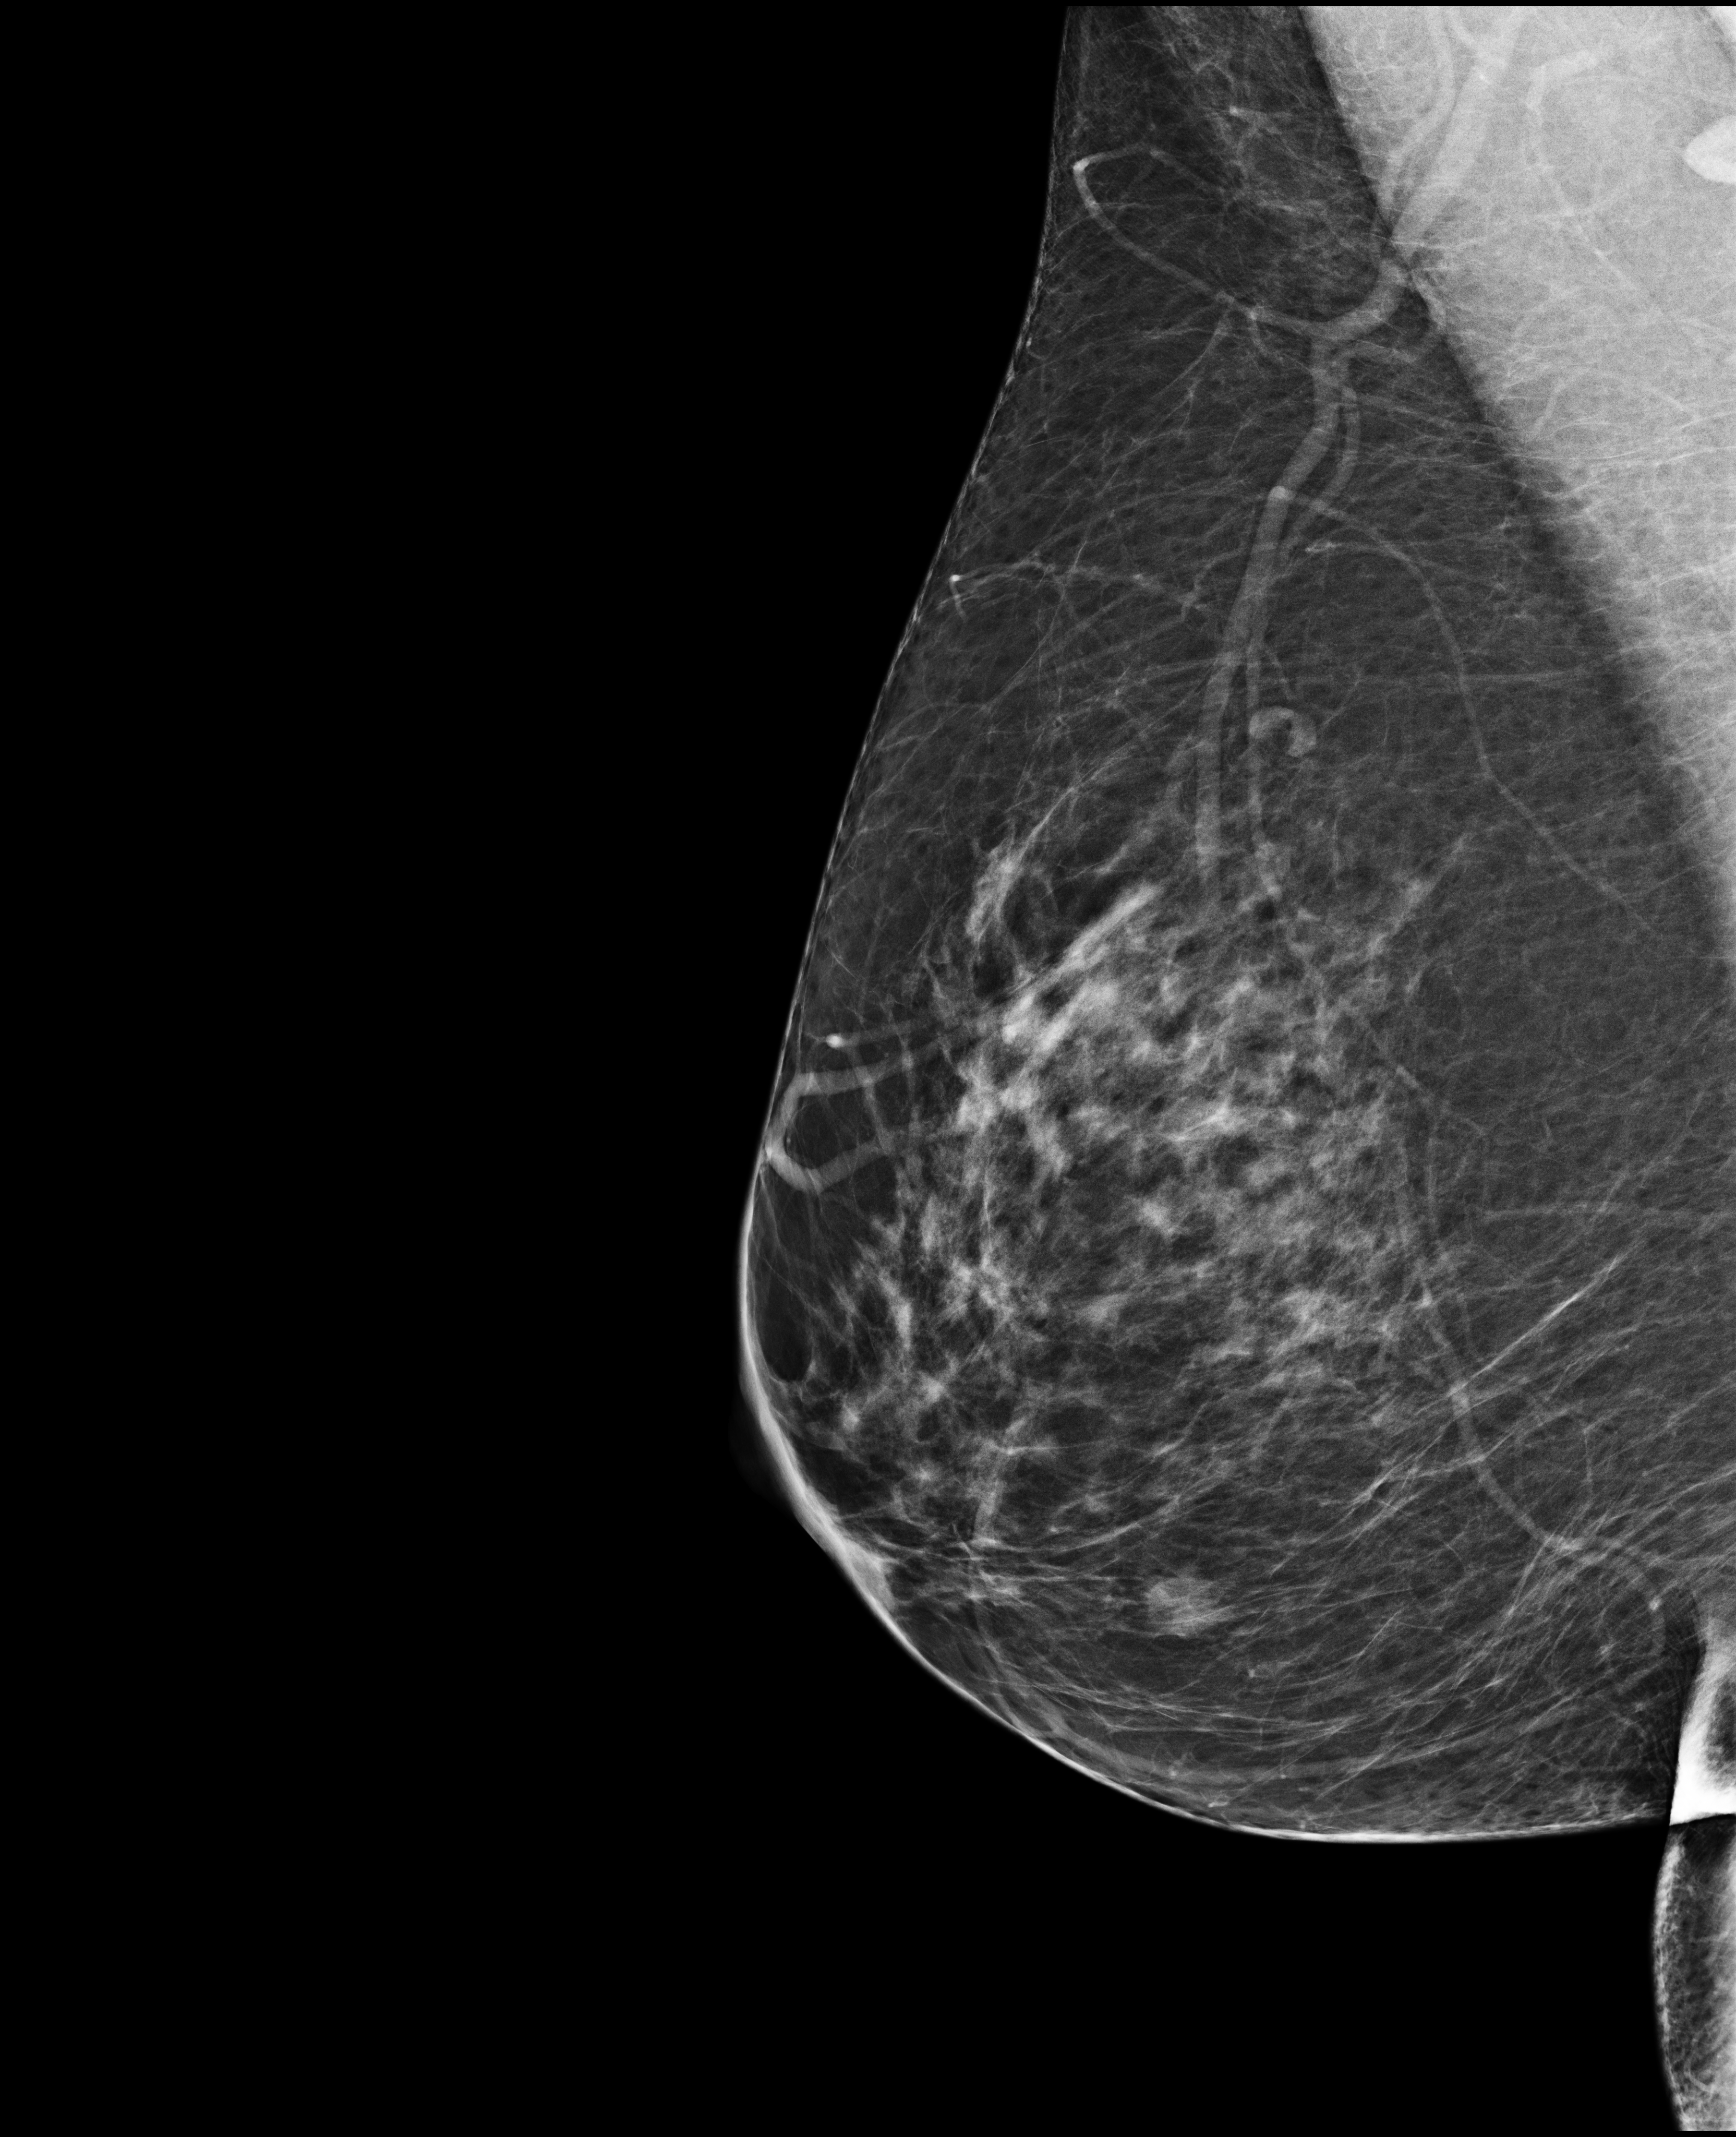
Screening examination, compressed breast thickness 78 mm. Patient aged 60 years (female).
Image type: full-field digital mammogram. Breast: right. Projection: medio-lateral oblique projection.